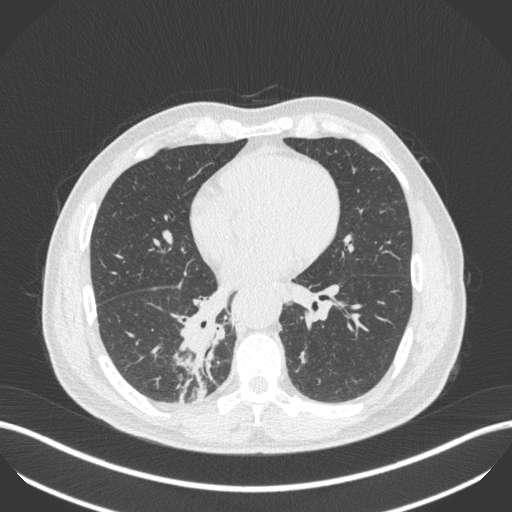
Chest CT, one axial slice; slice 212 of 451 in the series (ordered by position); 100 kVp; lung window (W 1500 / L -600 HU); 1 mm slice thickness; 512 × 512 image matrix, field of view 400 × 400 mm. Patient: male, 61 years. From the clinical record (not read from this slice): clinical TNM (as recorded): T1 N0 M0; histopathological grade: G3.
Outlined on this slice (bounding box drawn by a radiologist):
- lung tumour (recorded histology: small cell carcinoma): bounding box <177,323,216,402> (left, top, right, bottom; pixels)